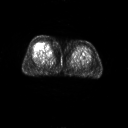
FDG PET of an extremity soft-tissue mass (from a PET/CT study), one axial slice. Position 21 of 267 along the scan axis. 3.27 mm slice thickness. 128 × 128 image matrix, field of view 700 × 700 mm. Patient: female, 56 years. Case-level facts recorded for this patient, not image findings: histological type: malignant solitary fibrous tumor; grade: intermediate; site of the primary tumour: right thigh.
Structures marked on this image (expert contour drawn on MRI and transferred to this co-registered scan by the dataset authors):
- gross tumour volume including surrounding oedema: box from (x=39, y=41) to (x=54, y=51) px